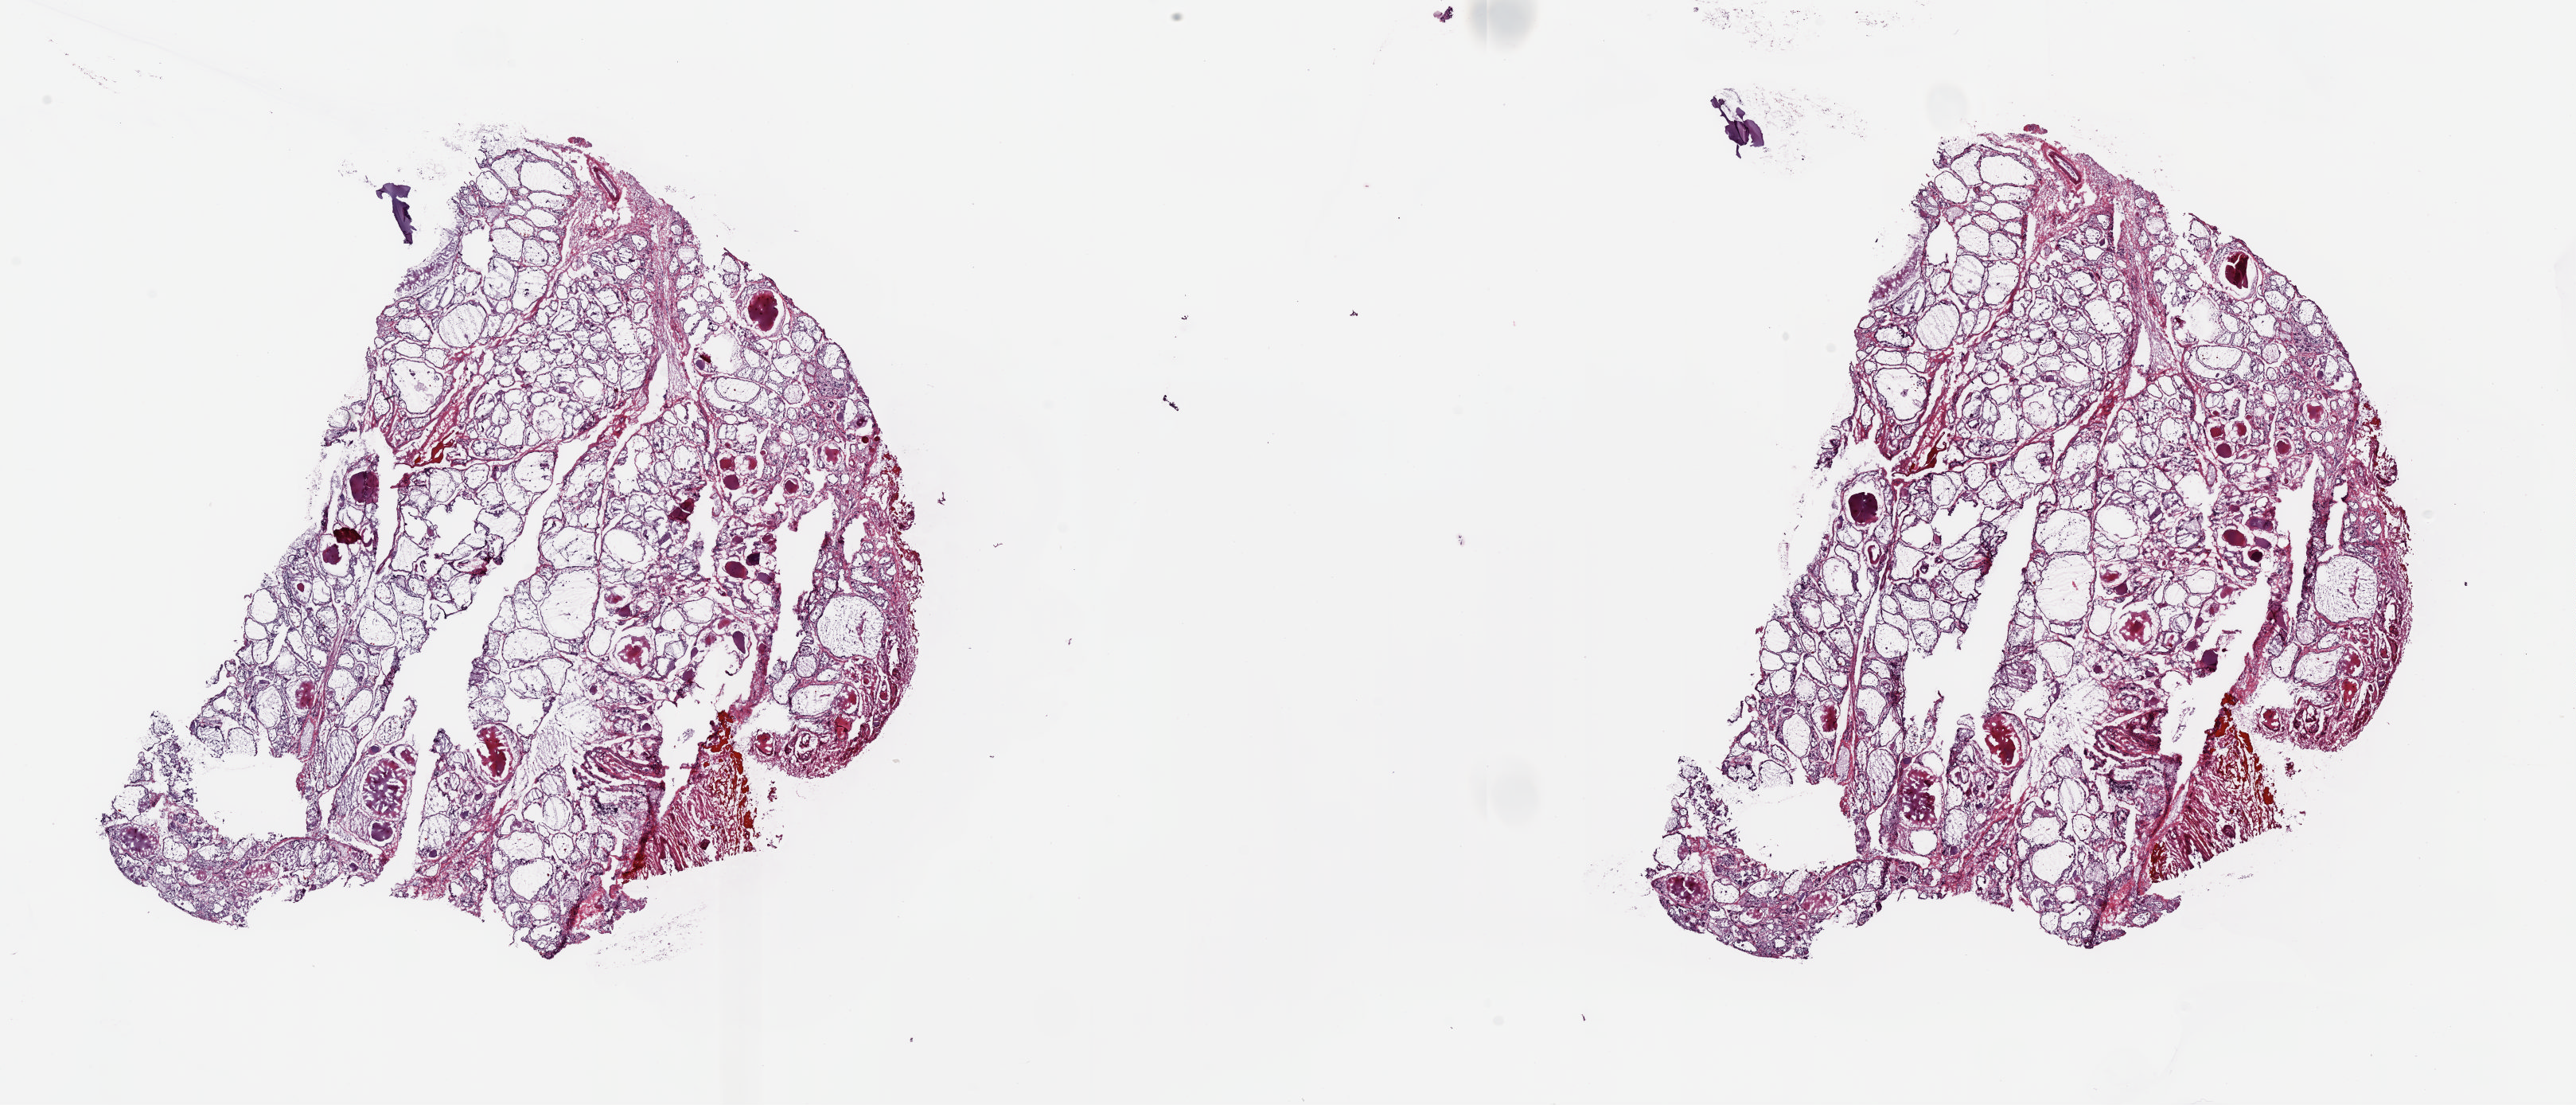
H&E whole-slide image — a low-resolution overview of the entire scanned area, about 25.6 x 11.0 mm. Frozen section. Sample: solid tissue normal (non-tumour tissue), thyroid. Patient: female, age at initial diagnosis 47 years. Slide review estimates, as recorded: tumour cells 0%, tumour nuclei 0%, normal cells 100%, stromal cells 0%, necrosis 0%. Inflammatory infiltration, as recorded: lymphocyte infiltration 0%, monocyte infiltration 0%, neutrophil infiltration 0%.
This section: solid tissue normal sample (biorepository sample class). Patient diagnosis: Papillary adenocarcinoma, NOS.